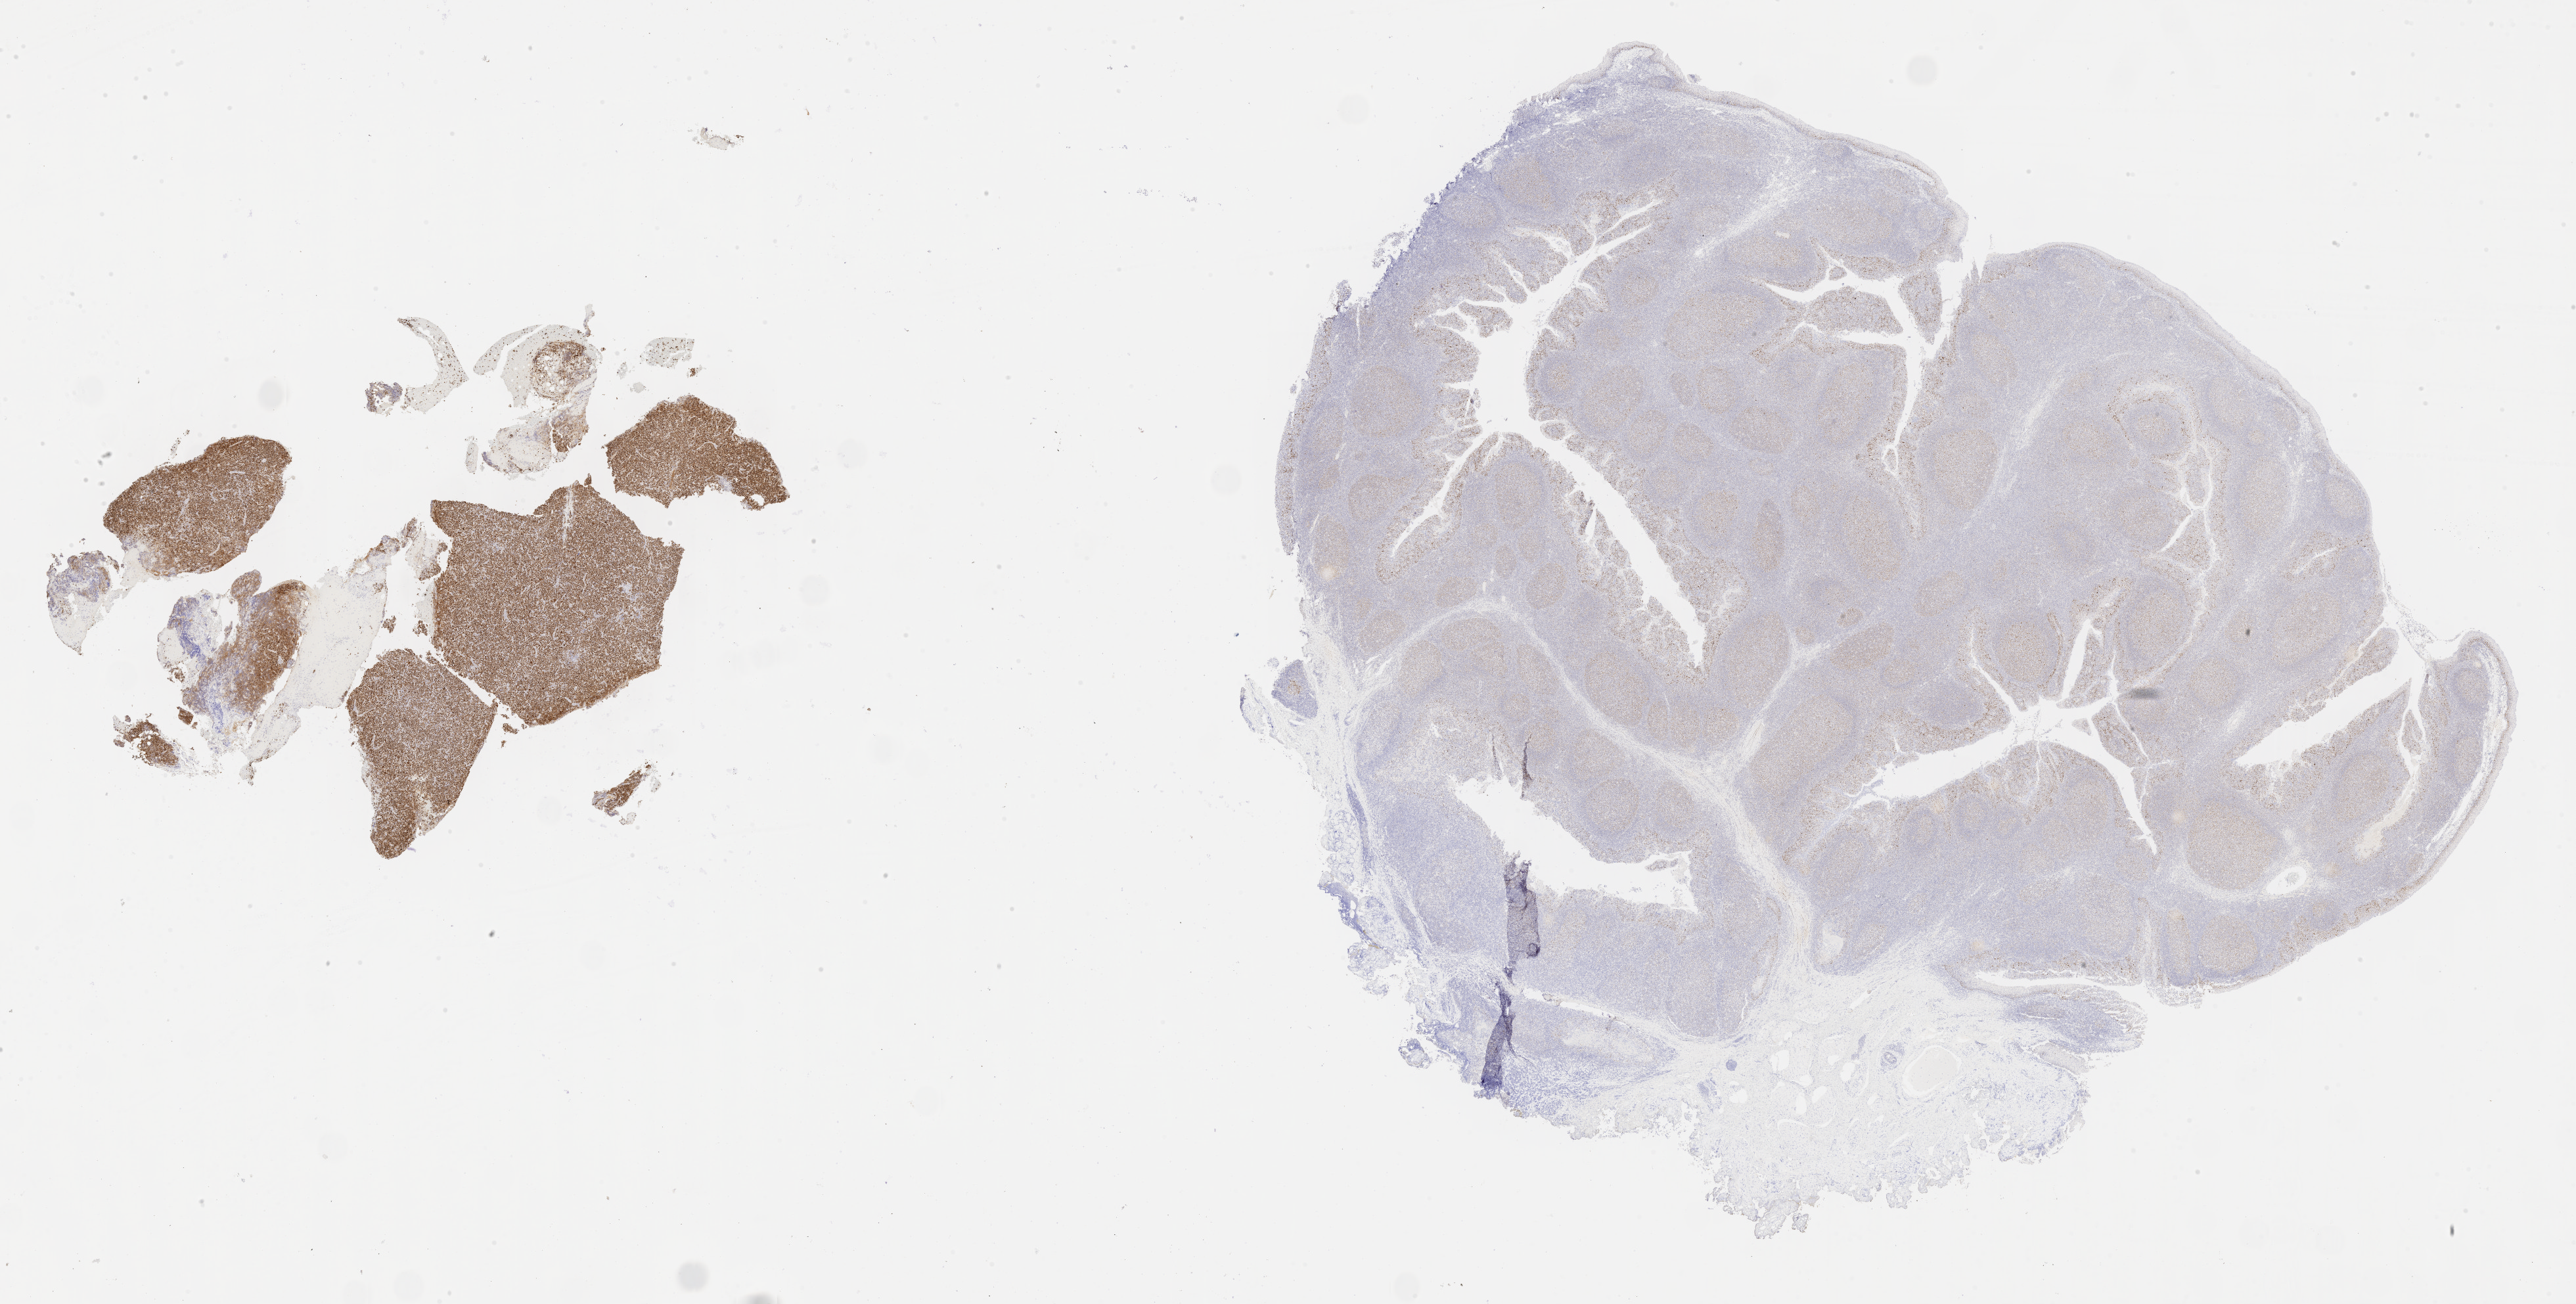
Immunohistochemistry (IHC) whole-slide image stained for p53, shown as a low-resolution overview of the whole scanned area (about 31.7 x 16.0 mm); specimen: tumor tissue; anatomic site: lymph node. Patient: female, age 71 years.
Diagnosis: Diffuse large B-cell lymphoma, NOS.